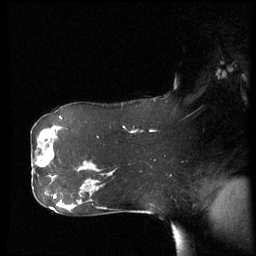
Breast MRI (dynamic contrast-enhanced), one sagittal slice. Position 40 of 60 along the scan axis. Dynamic contrast-enhanced series, image 2 of 3 at this slice position (ordered by acquisition). 1.5 T. TE 4.2 ms, TR 8.4 ms. 2.9 mm slice thickness. 256 × 256 image matrix, field of view 280 × 280 mm. Patient: female, 61 years. From the clinical record (not read from this slice): setting: breast cancer imaged before/during neoadjuvant chemotherapy; receptor status: HR-positive, HER2-negative.
Outlined on this slice (semi-automatically segmented with operator editing):
- analysis volume of interest (the breast-tissue region the enhancement analysis was run in; not a lesion): bounding box [x1, y1, x2, y2] px = [32, 142, 58, 179]
- tumour enhancement mask (voxels above the 70 % enhancement threshold inside the analysis volume of interest): [38, 162, 51, 167]